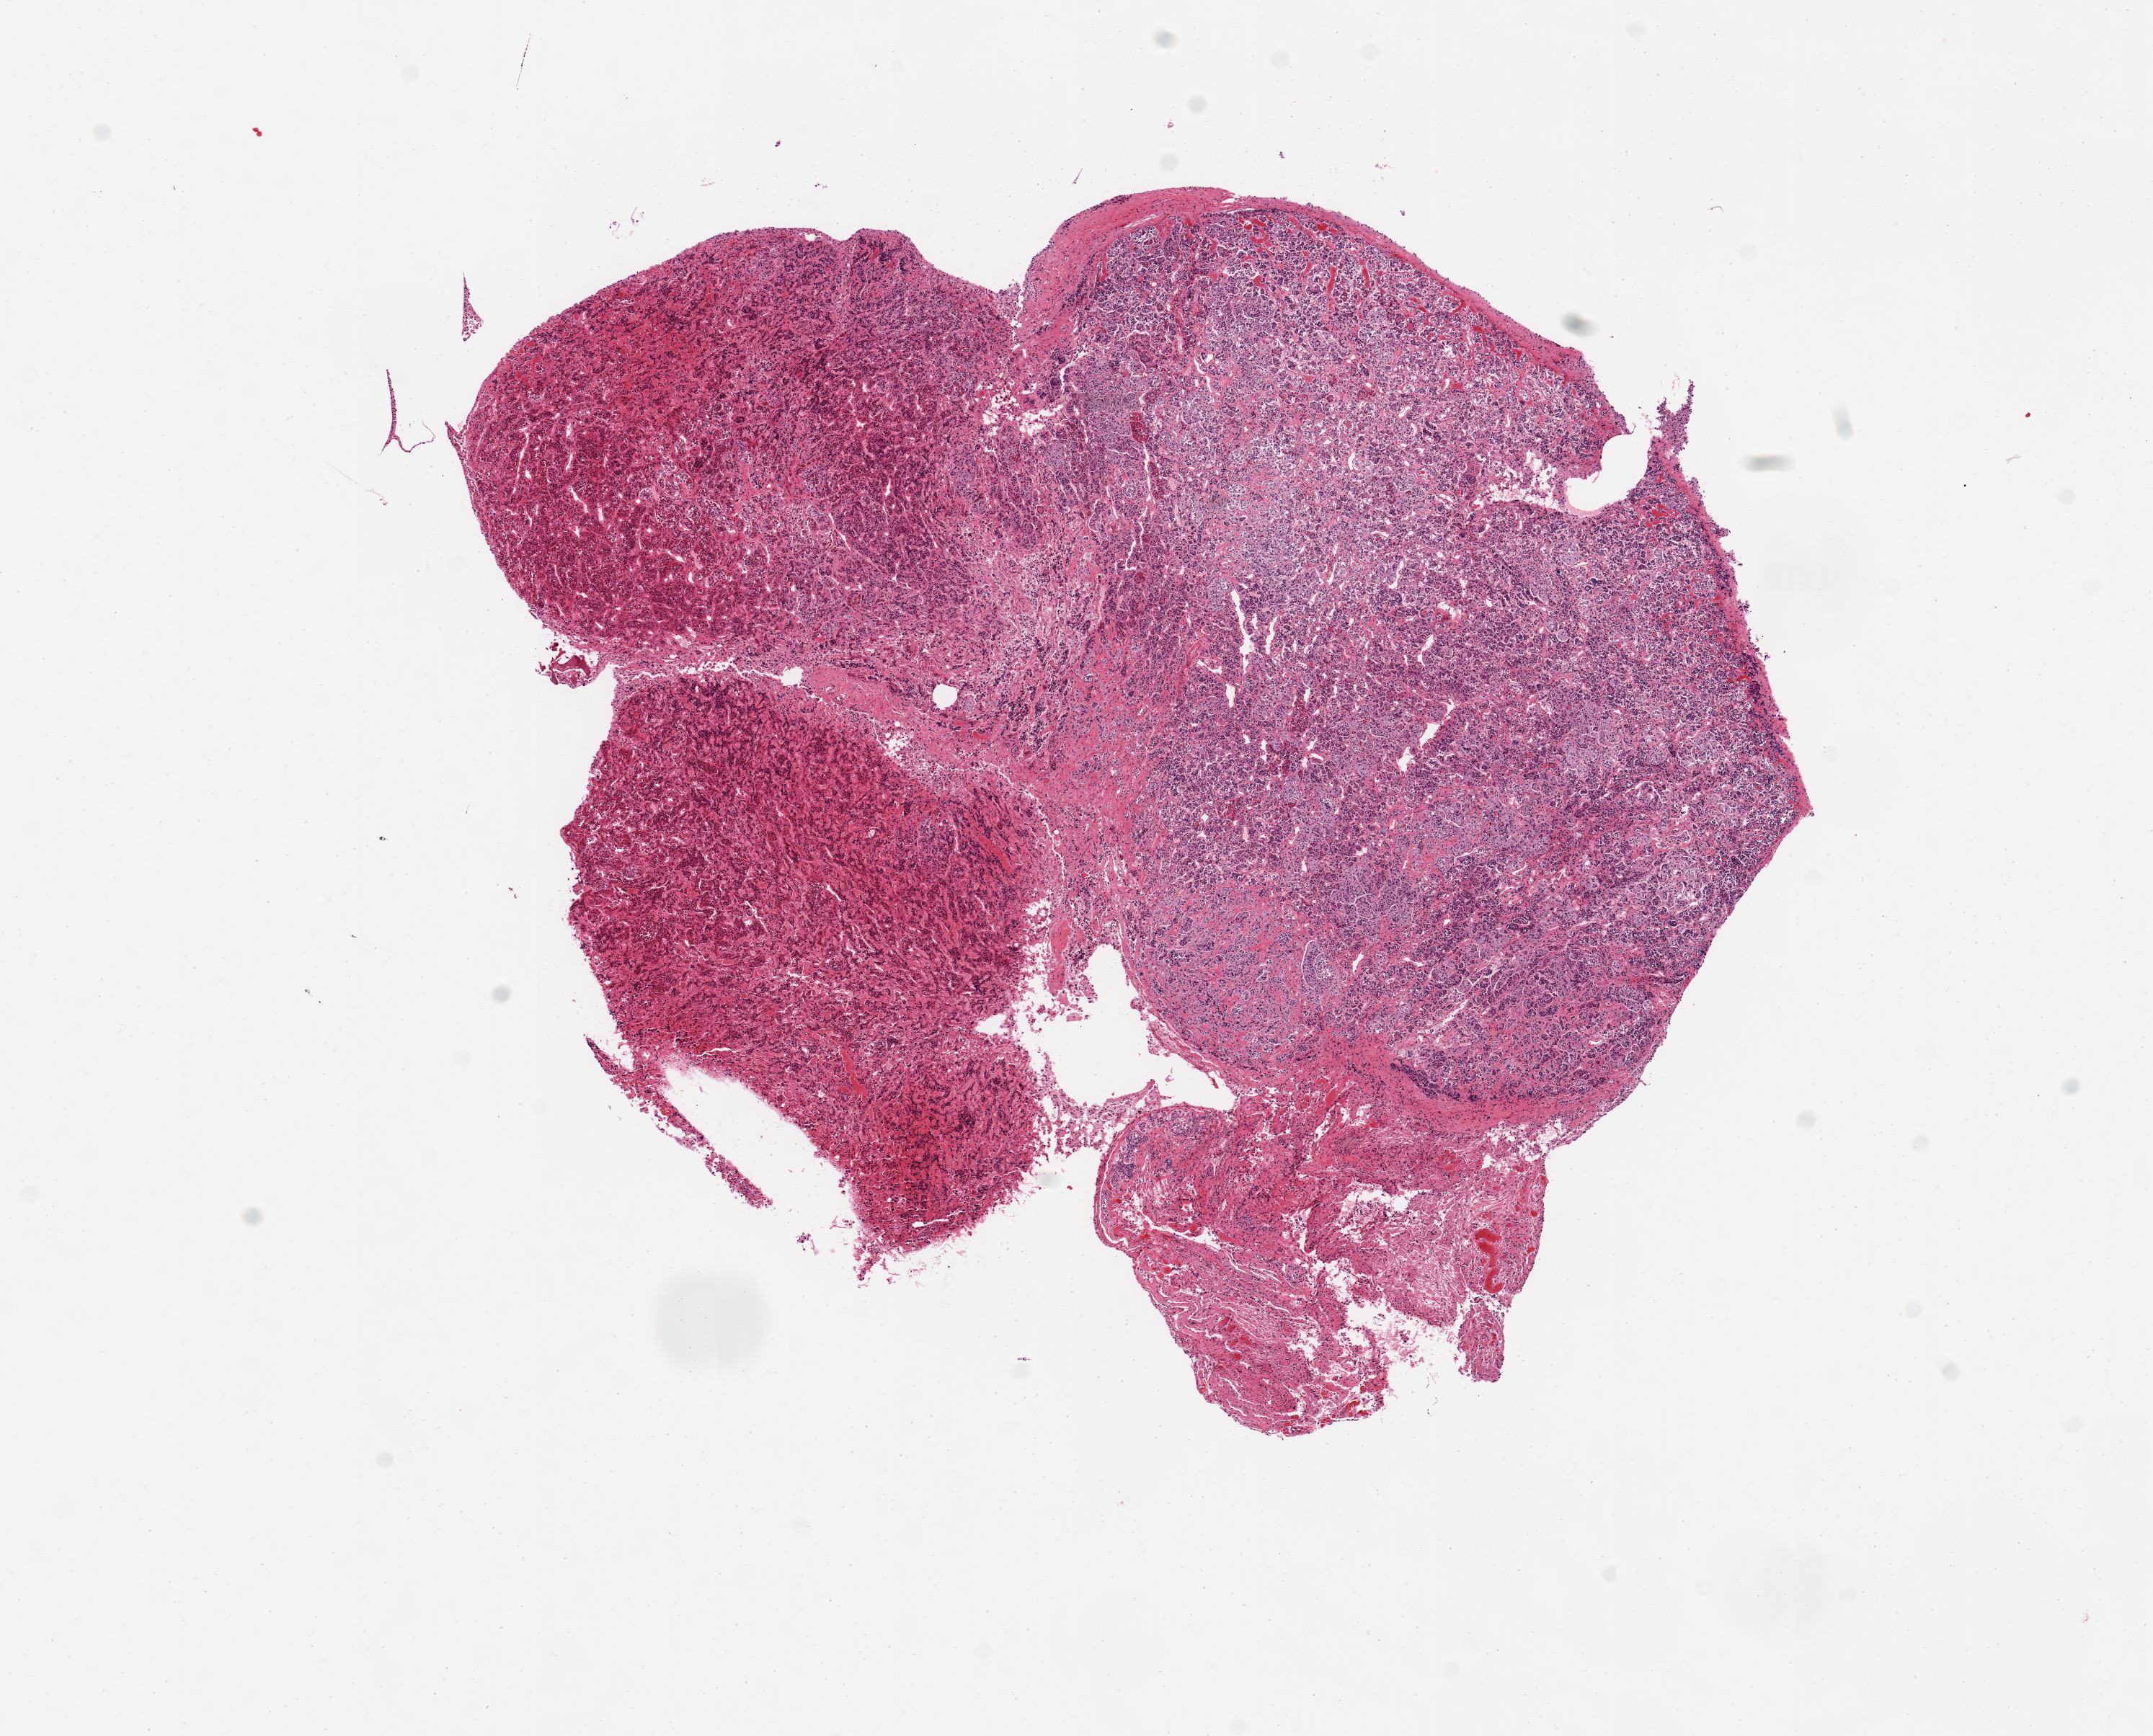
Digitized hematoxylin and eosin (H&E)-stained section, shown as a low-resolution overview of the whole scanned area (about 11.8 x 9.5 mm, acquisition: 20x scan). PAXgene-fixed, paraffin-embedded tissue. Section of pituitary (target tissue). Tissue donor sample. Donor sex: male.
- reviewer comment on this tissue sample: 1 pieces